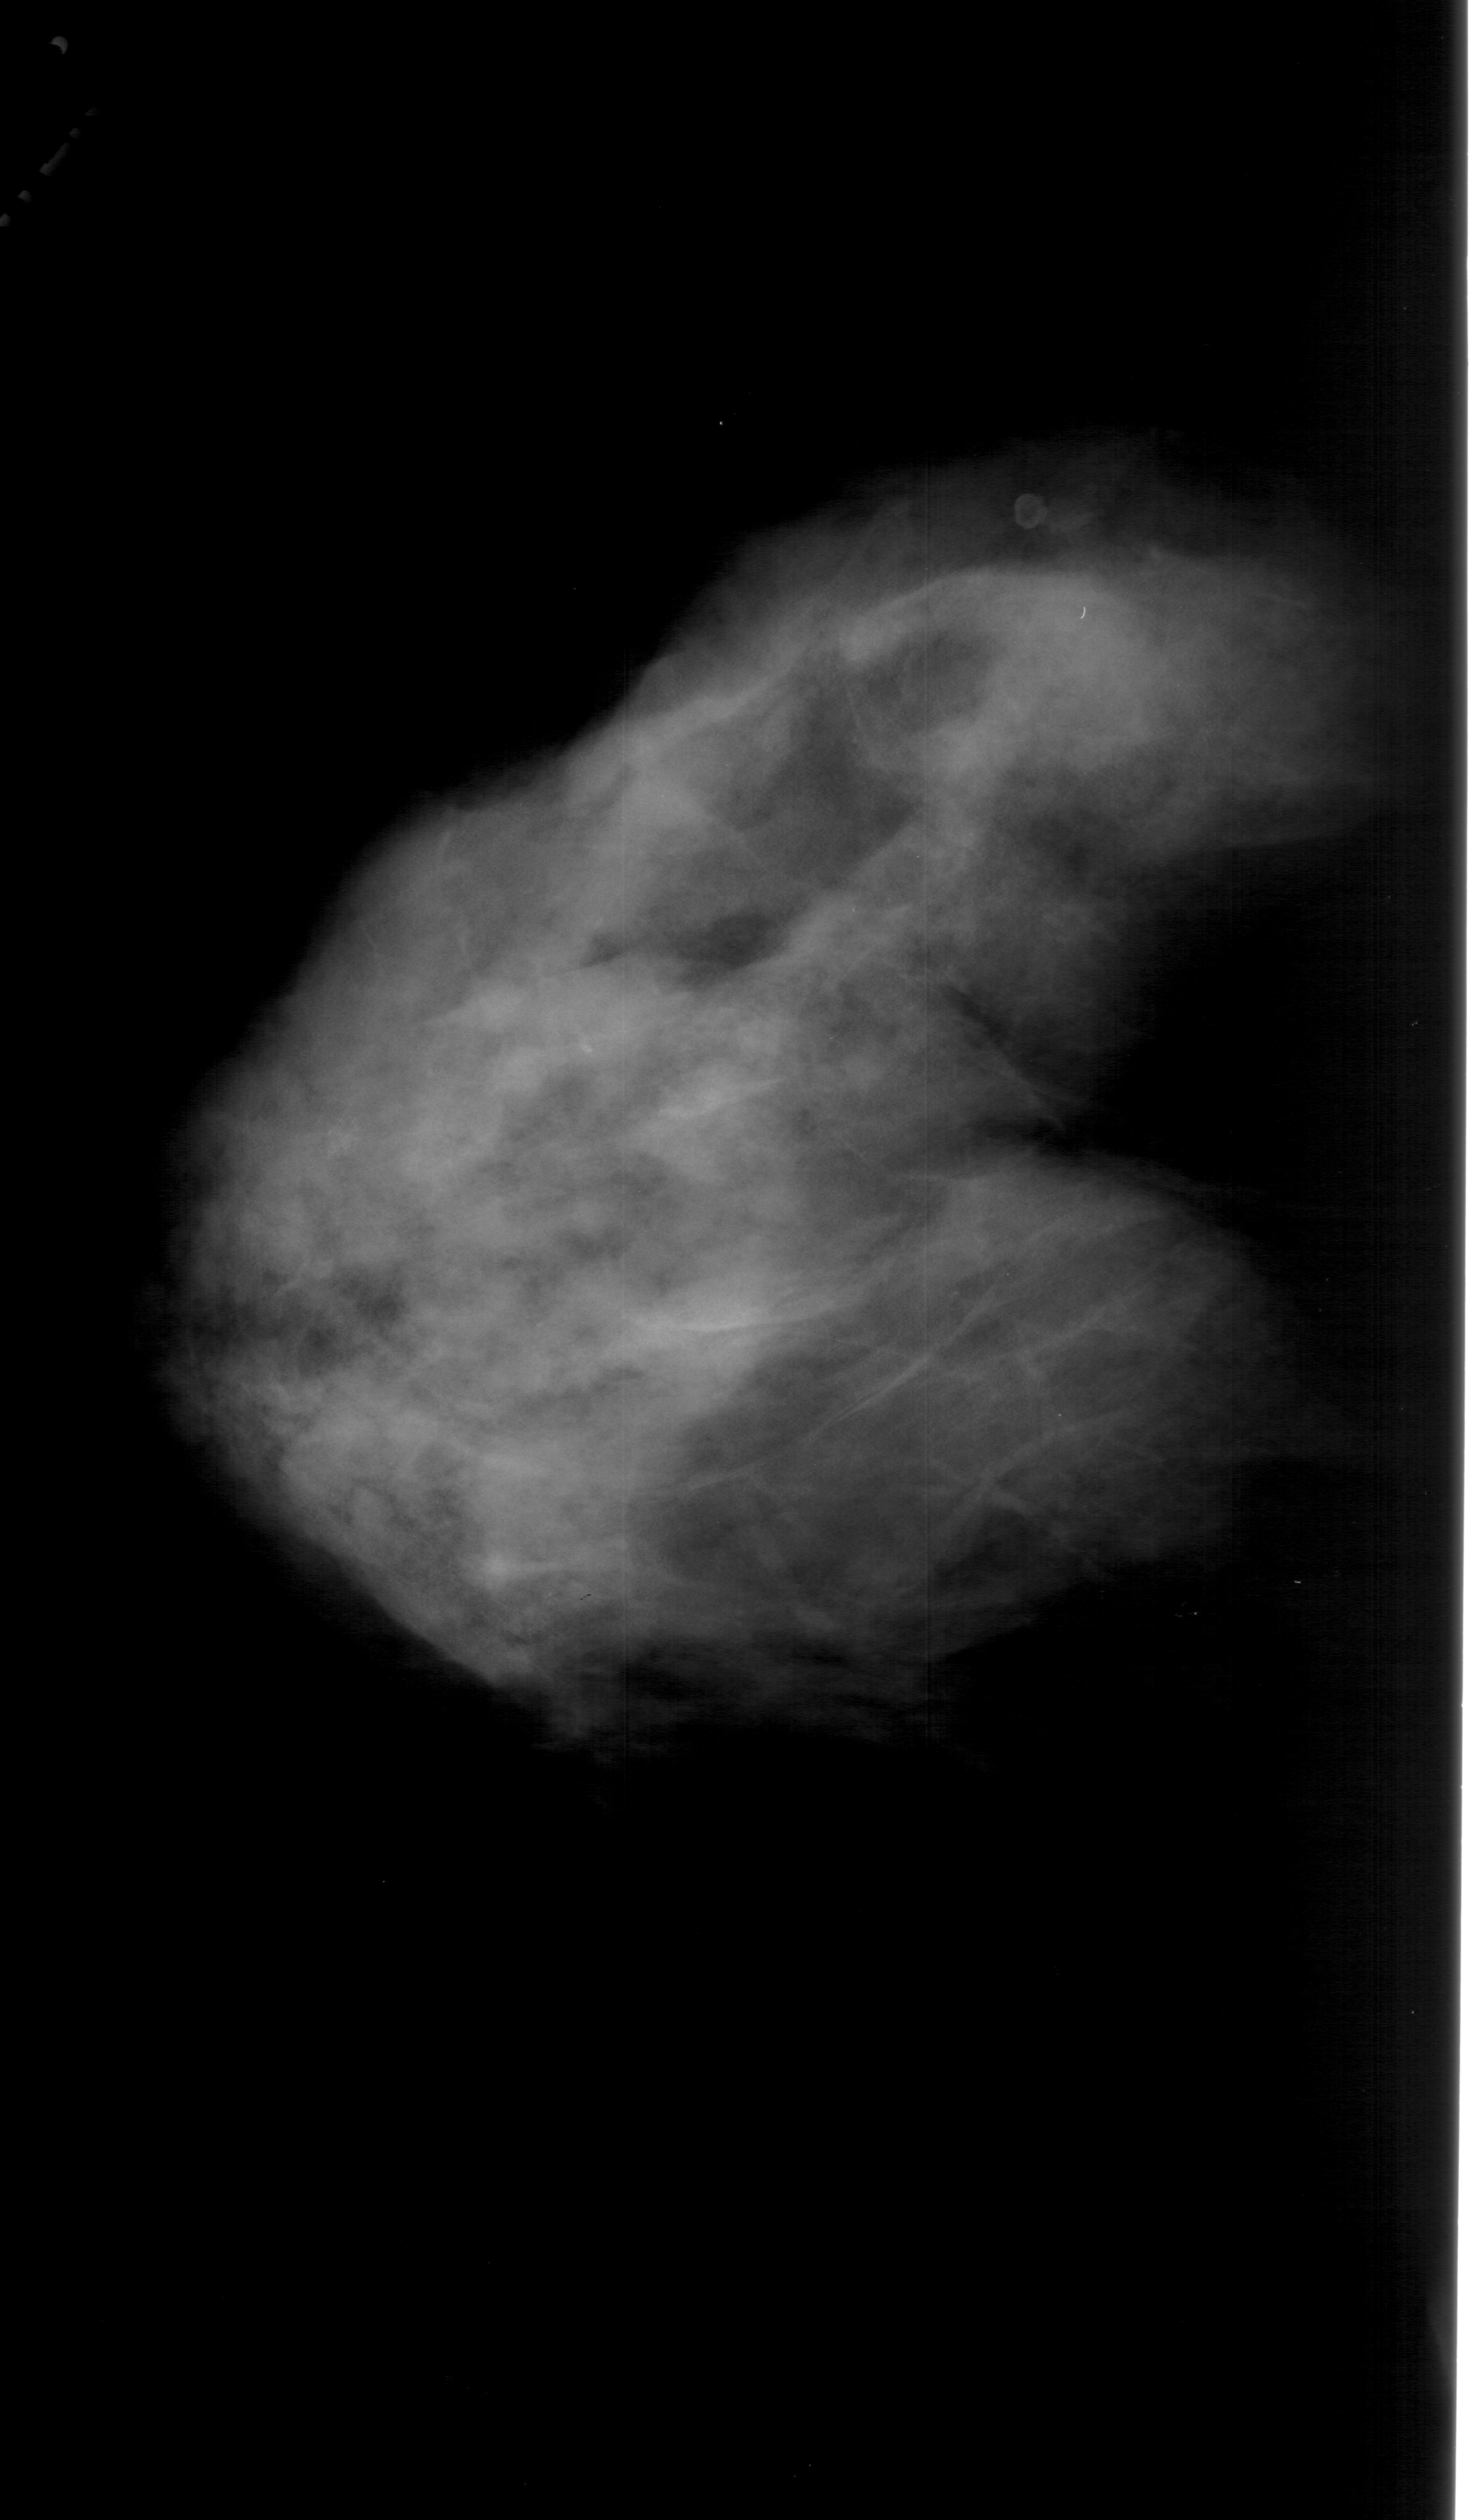
Digitized screen-film mammogram; left breast; CC view; BI-RADS breast density category 4 (scale 1–4); 1476 × 2520 image matrix.
Expert-marked regions of interest on this image (one box per marked abnormality):
- calcifications, morphology pleomorphic, distribution clustered; BI-RADS assessment category 4; pathology (as recorded): malignant: bounding box [x1, y1, x2, y2] px = [313, 1102, 383, 1177]